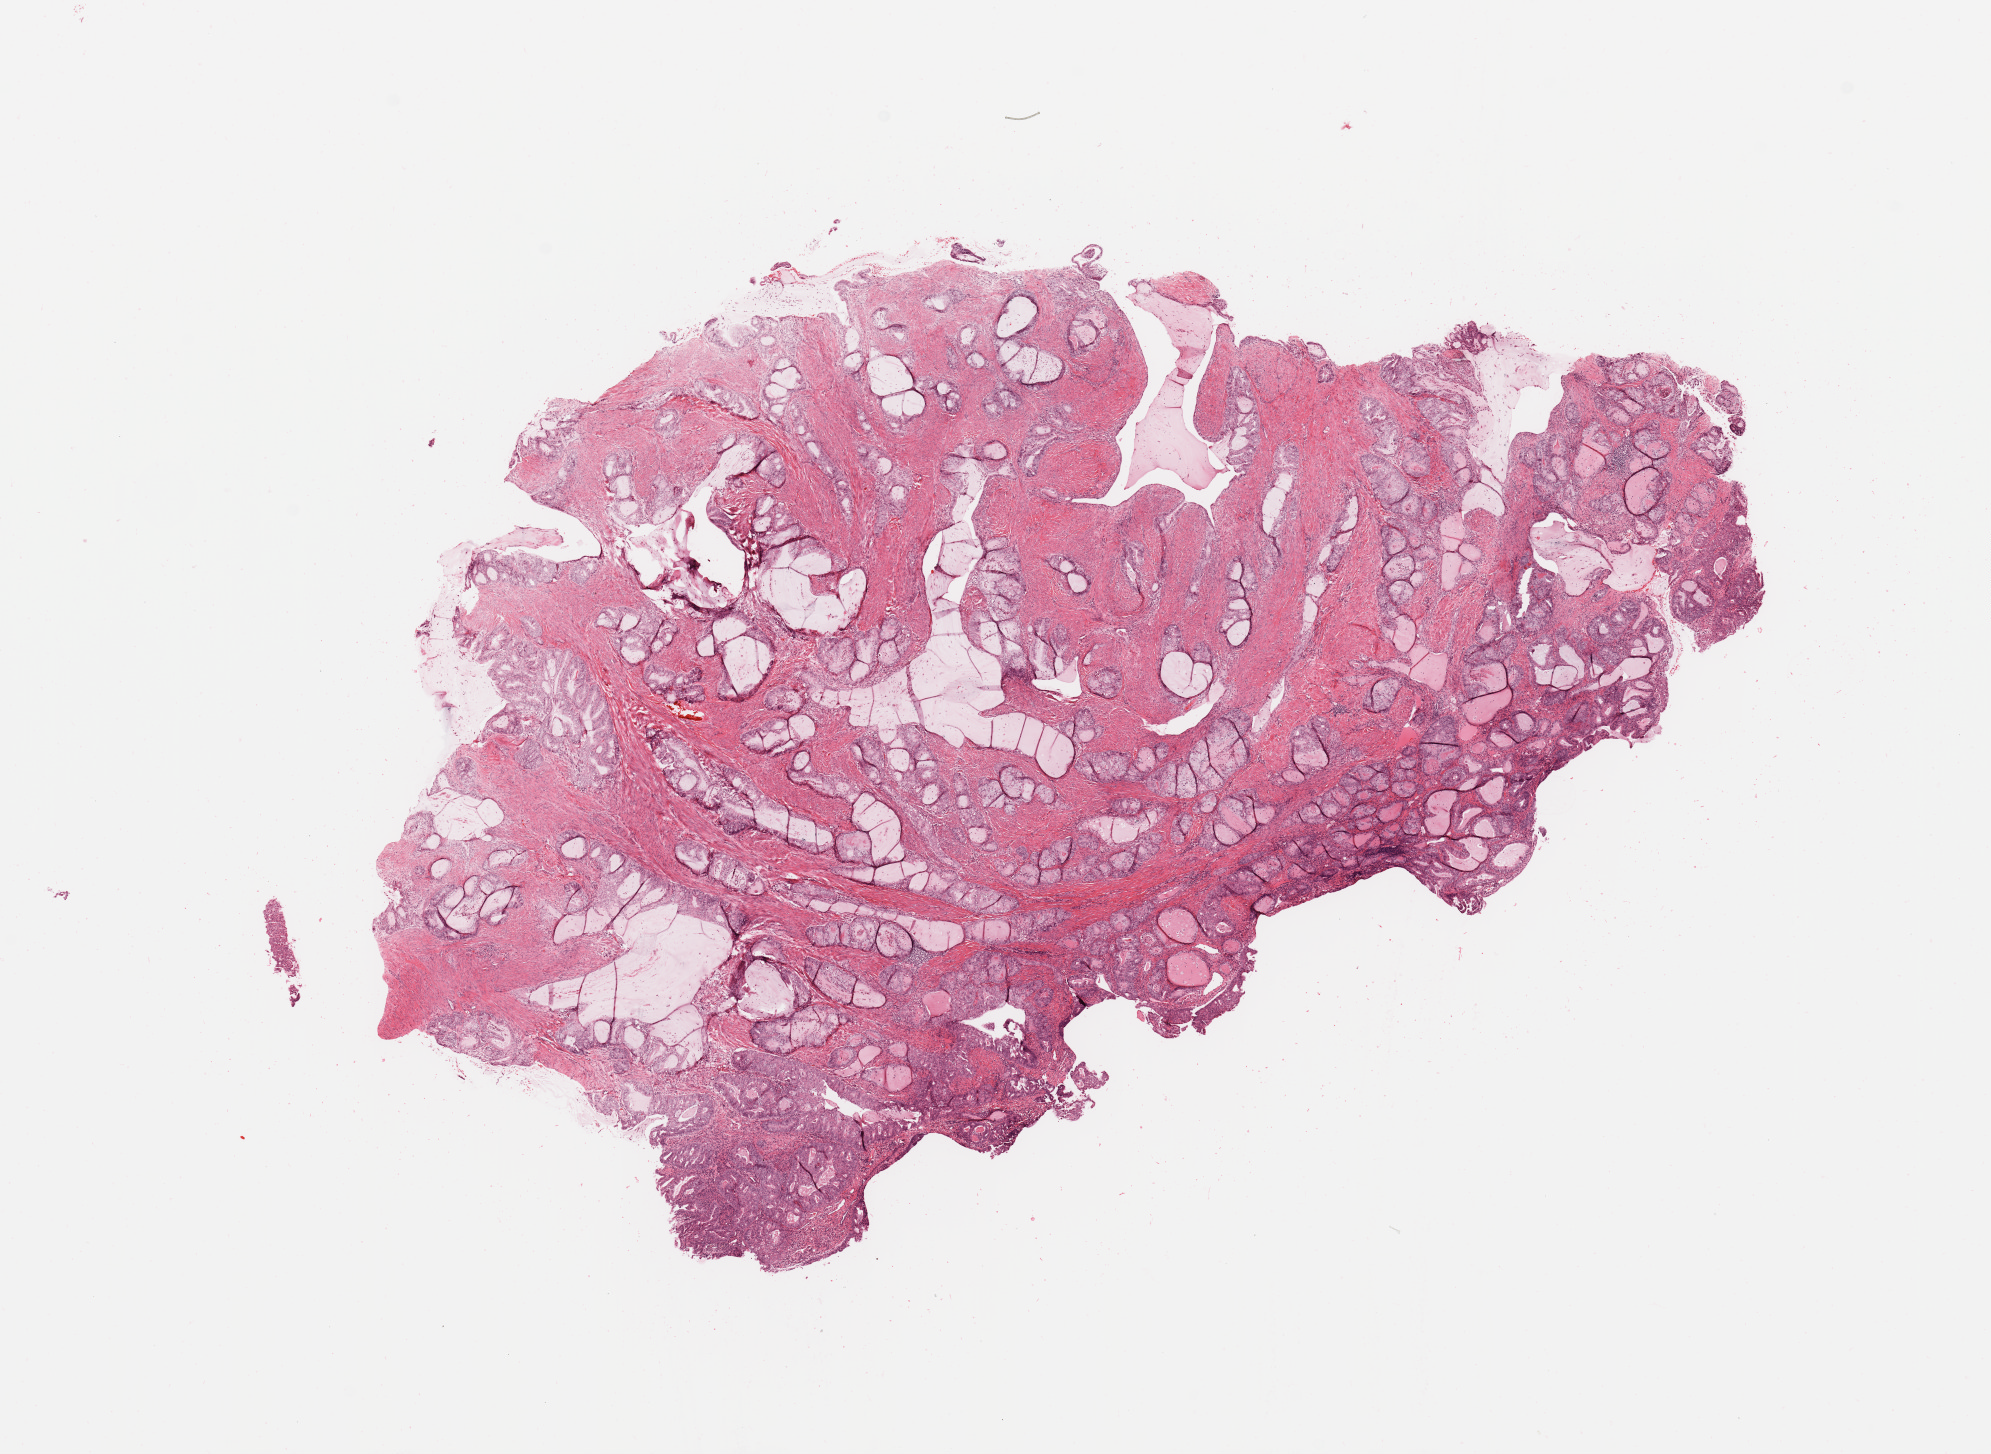
Digitized H&E tissue section (whole slide) — low-resolution overview of the scanned area, about 15.8 x 11.5 mm (slide scanned at 20x); normal (non-tumour) tissue sample, sampled site: uterus. Female, 74 y/o.
This section: normal (non-tumour) tissue from the same patient. Patient diagnosis: Endometrioid adenocarcinoma, NOS.